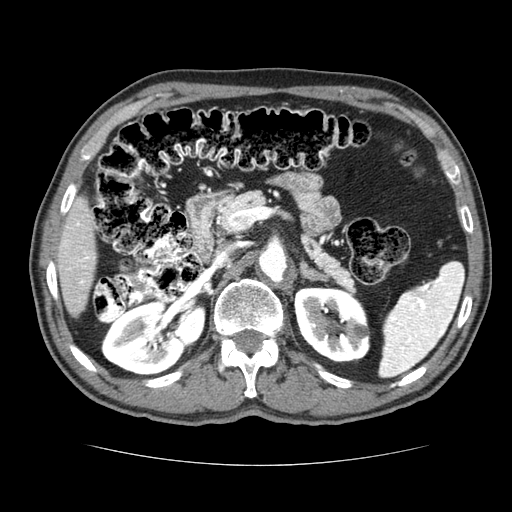
Contrast-enhanced abdominal CT (liver protocol), one axial slice. Slice 34 of 79 in the series (ordered by position). 120 kVp. Soft-tissue window (W 400 / L 40 HU). 512 × 512 image matrix. Case-level facts recorded for this patient, not image findings: diagnosis: hepatocellular carcinoma (patient treated with transarterial chemoembolisation; whether this scan precedes or follows treatment is not stated here); TNM stage (as recorded): Stage-I; Child-Pugh class: A.
Annotated regions visible in this slice (semi-automatically segmented with operator editing):
- liver parenchyma outside the tumour (the mass and vessels are separate outlines, so this box may not span the whole liver): bounding box (x1, y1, x2, y2) in pixels: (56, 196, 96, 316)
- liver vessels: (63, 221, 90, 284)